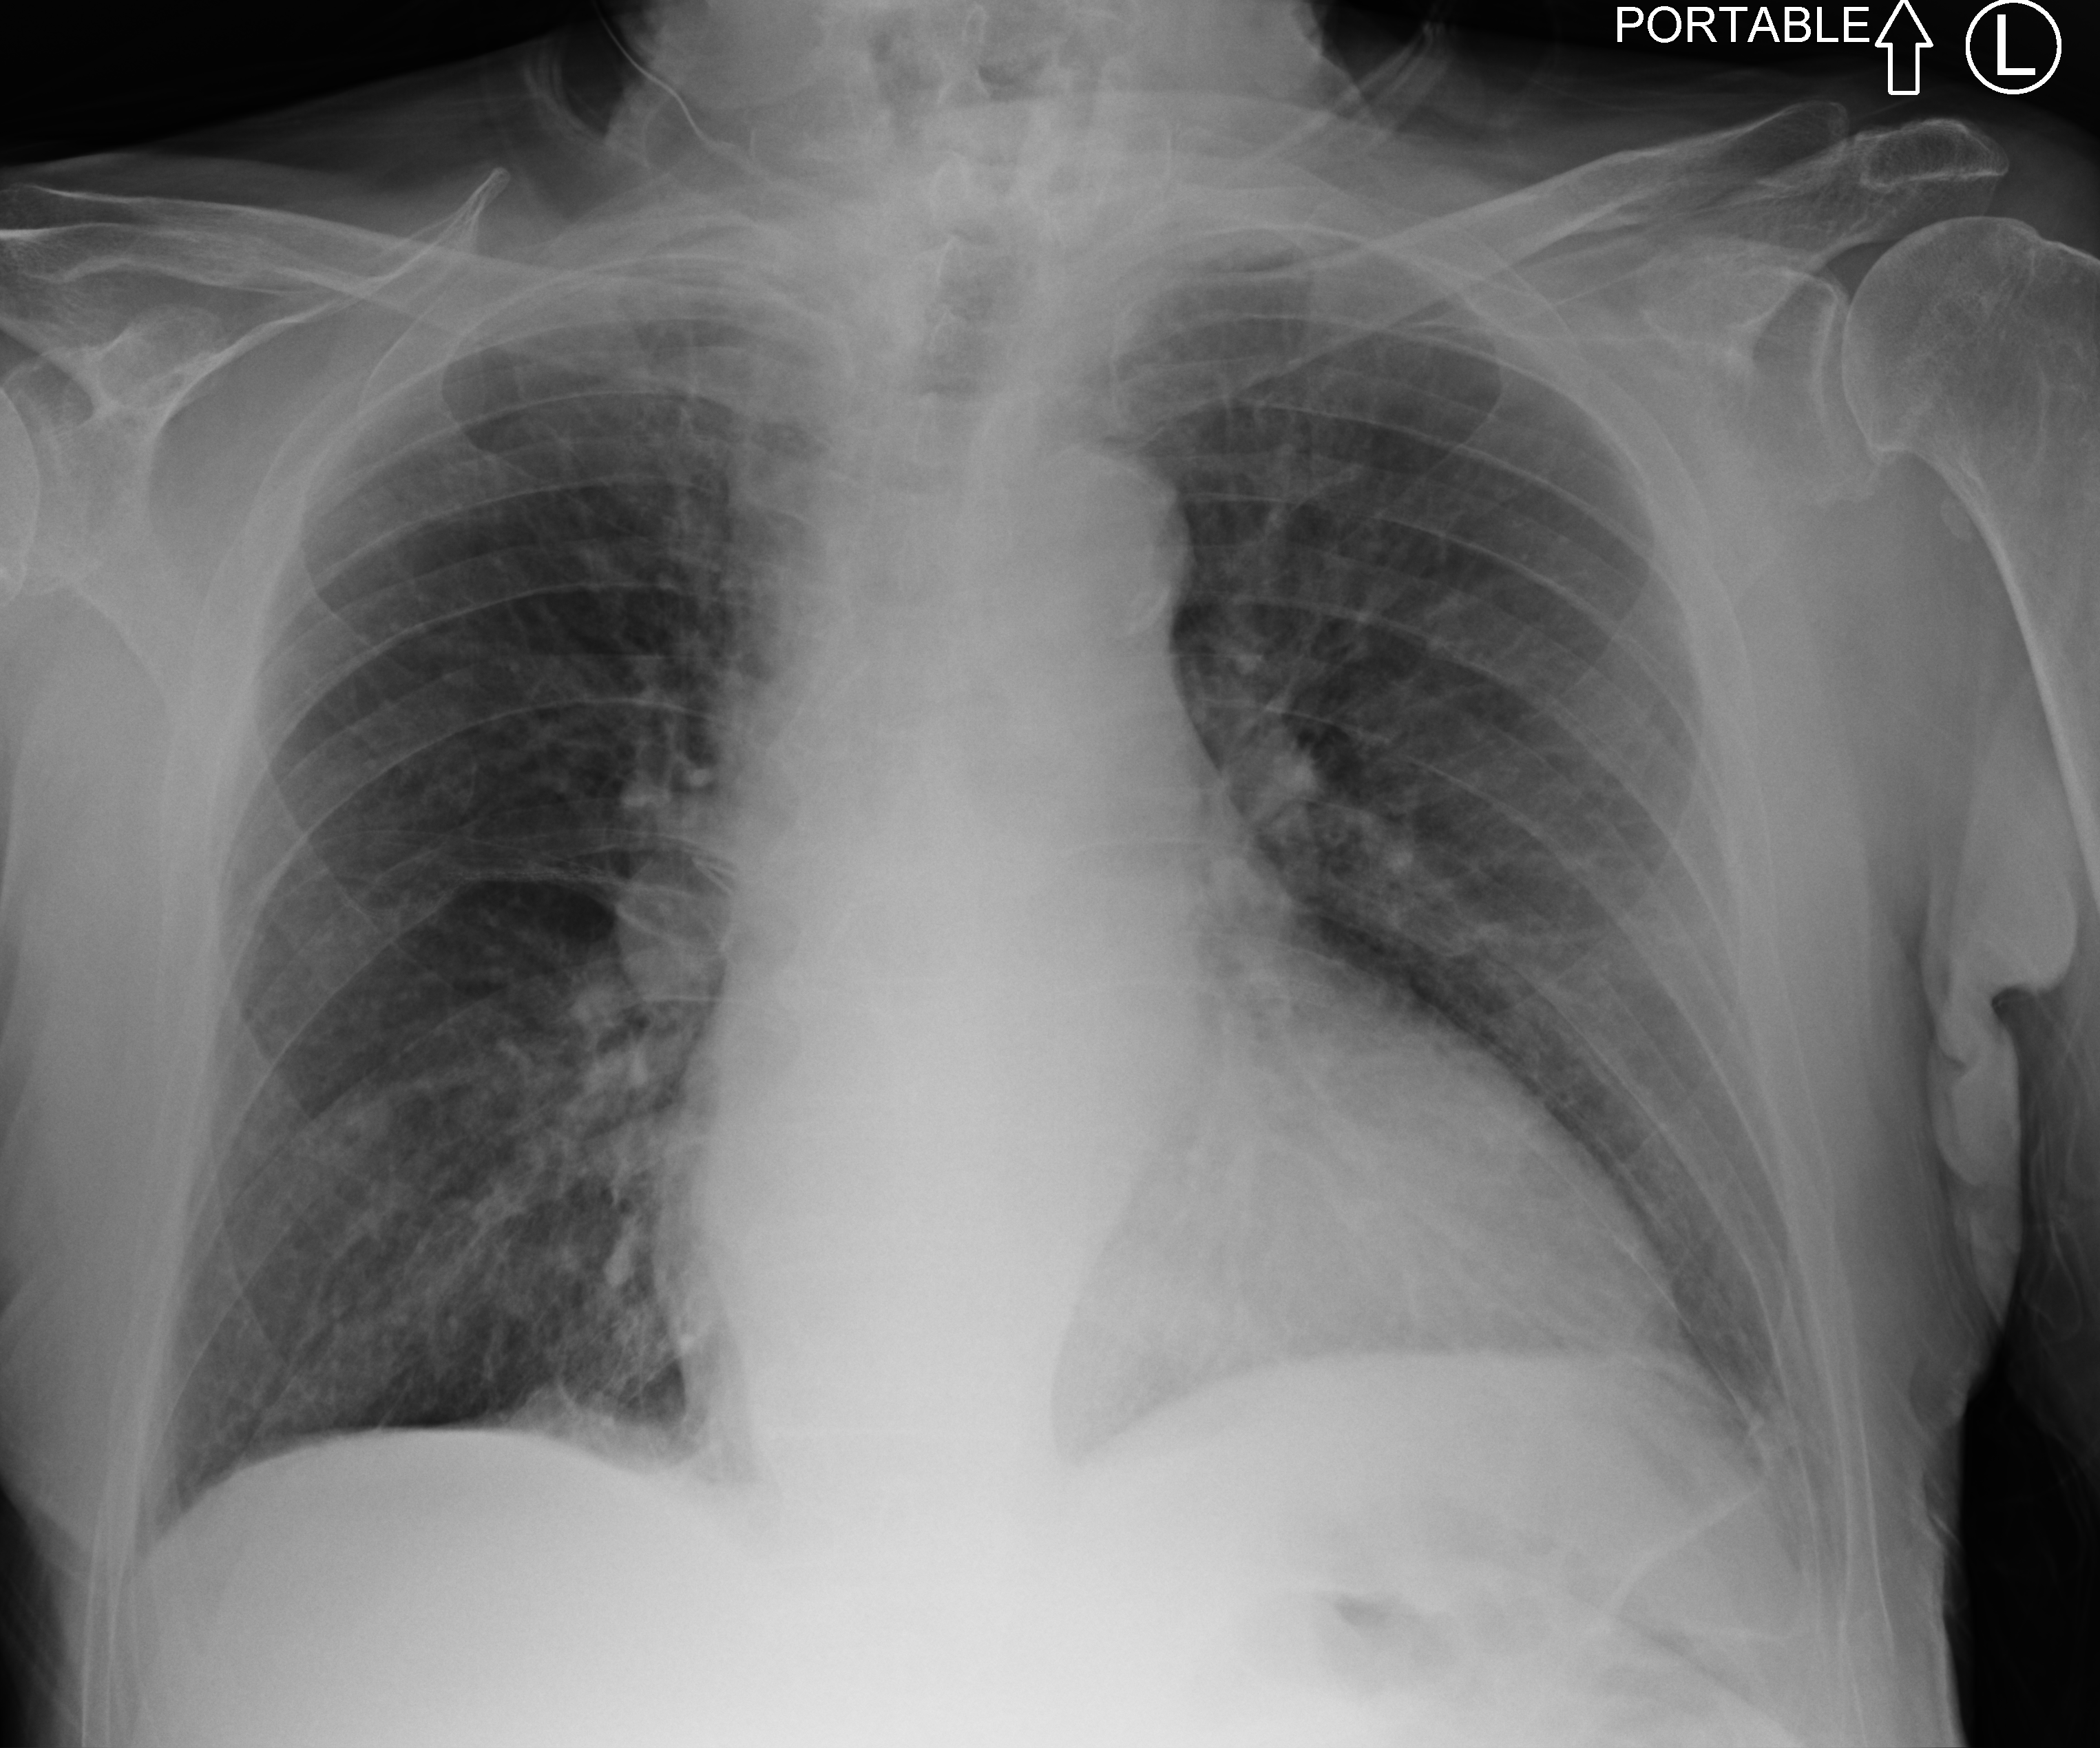
Portable chest radiograph; anteroposterior (AP) projection. Male patient hospitalised with COVID-19, age 75–90 years.
From the hospital-stay record, not from the radiograph (when in the stay this image was taken is not recorded): length of hospital stay: 3 days; admitted to intensive care during this hospital stay: no.